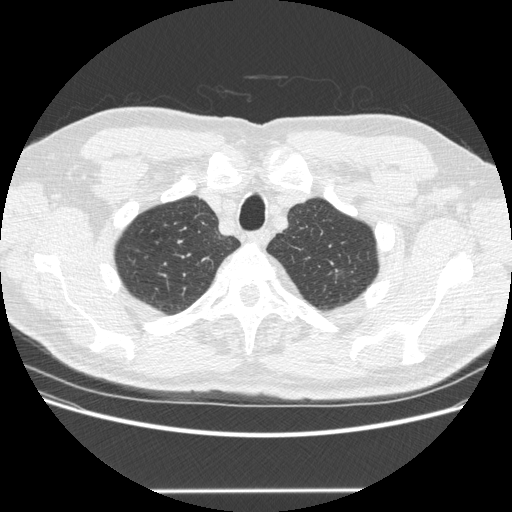
Chest CT (low-dose screening protocol), one axial image. Second screening round (one year after baseline). Lung window (W 1500 / L -600 HU). 1.25 mm slice thickness. Standard (soft-tissue) reconstruction kernel (STANDARD). Slice 50 of 223 in the series. 512 × 512 image matrix, field of view 380 × 380 mm. Male, age 69 years at enrolment. Former smoker at enrolment.
Expert-annotated lung lesion, bounding box <311,261,347,294> (left, top, right, bottom; pixels). Screening reader's record for this exam: no non-calcified nodule ≥4 mm recorded. Official screen result: negative screen, significant abnormalities not suspicious for lung cancer.